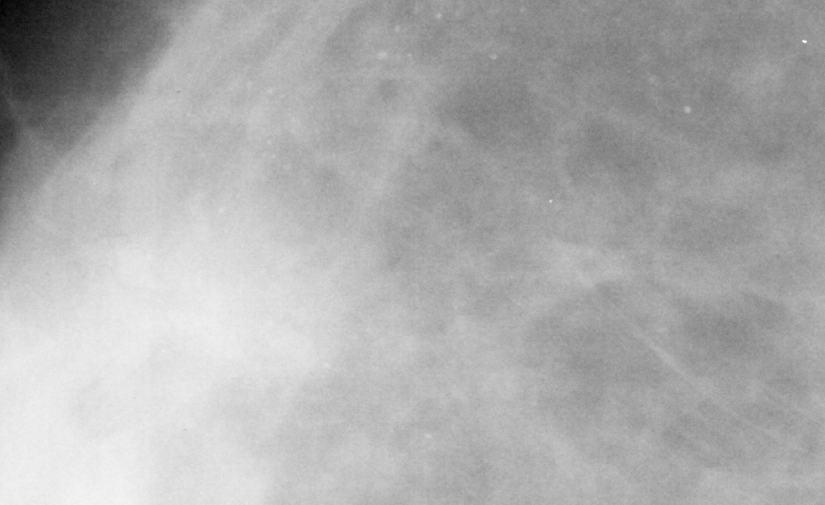
Crop from a digitized film mammogram around one marked abnormality; right breast; CC view.
Finding: calcifications, morphology pleomorphic, distribution segmental; BI-RADS assessment category 4; pathology result (as recorded, not read from the image): benign.